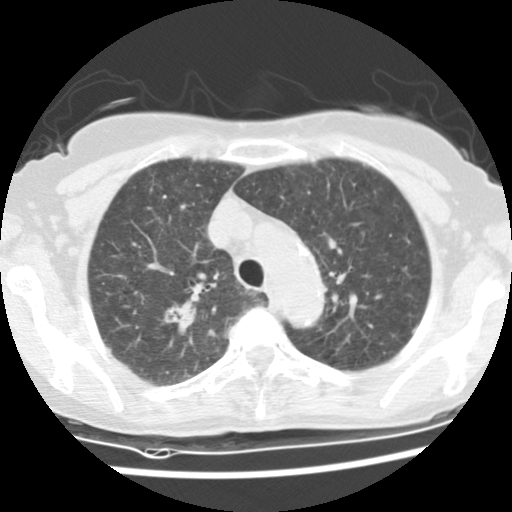
Axial slice from a low-dose chest CT screening exam, baseline annual screen, lung window (W 1500 / L -600 HU), 2.5 mm slice thickness, standard (soft-tissue) reconstruction kernel (STANDARD), 512 × 512 image matrix. Female participant, aged 66 years at enrolment.
- Expert-annotated lung lesion, box from (x=150, y=293) to (x=198, y=339) px.
- Reader record for this screening exam (exam-level; its link to the box is not recorded): non-calcified nodule or mass ≥4 mm, right upper lobe, 13 × 11 mm, soft tissue attenuation.